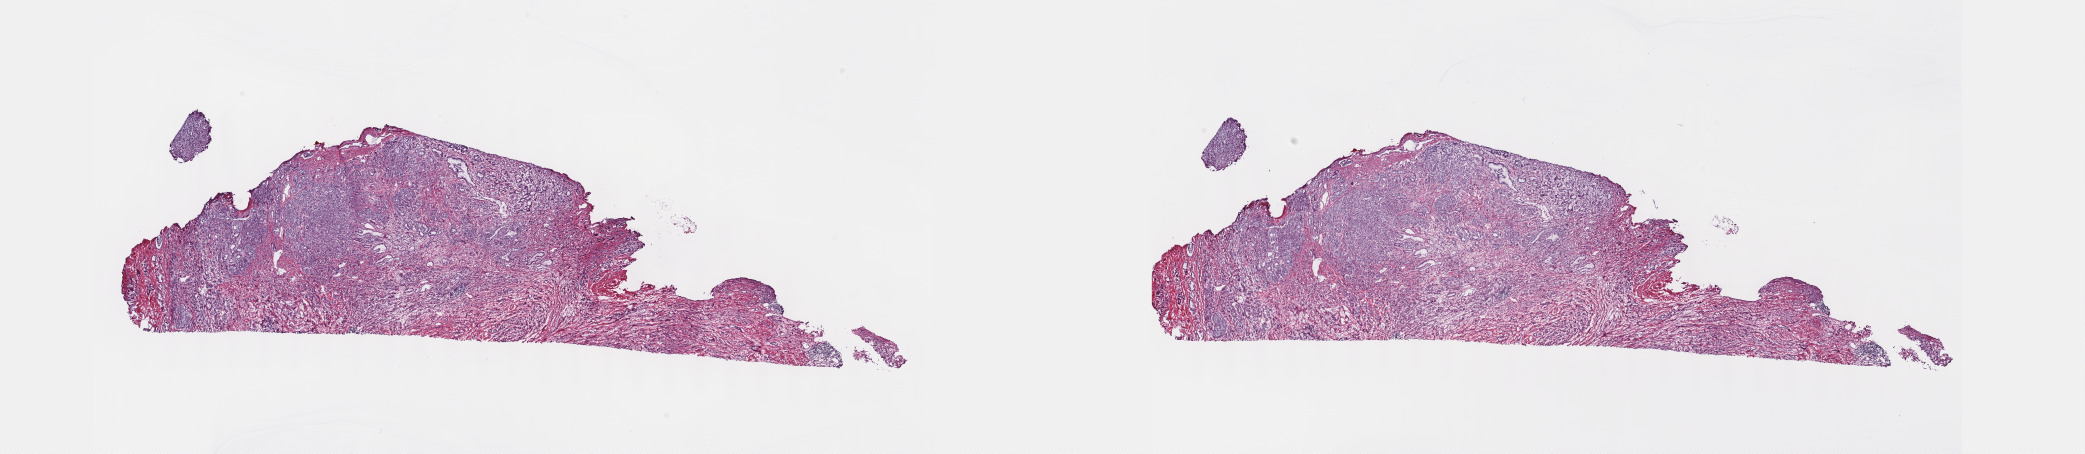
Digitized H&E-stained tissue section (whole slide), whole scanned area (about 33.7 x 7.3 mm, from a 40x scan) shown as a low-resolution overview; frozen section from the top of the tissue portion; sample: primary tumour, prostate. Patient: male, age at initial diagnosis 61 years.
Histologic diagnosis: Adenocarcinoma, NOS (prostate gland).